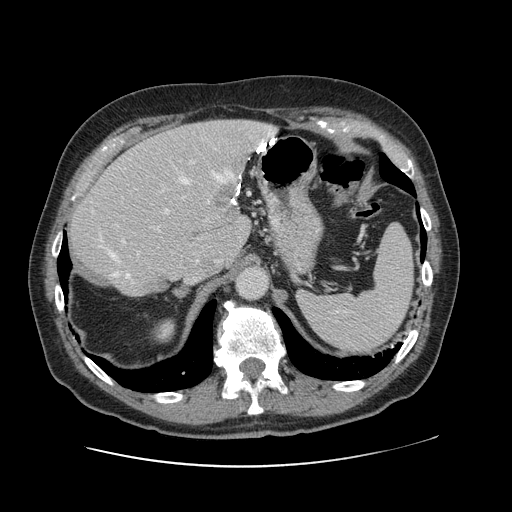
Contrast-enhanced abdominal CT, one axial slice; slice 82 of 138 in the series (ordered by position); 120 kVp; intravenous contrast given; soft-tissue window (W 400 / L 40 HU); 2.5 mm slice thickness; 512 × 512 image matrix. Male patient, age 71 years. From the clinical record (not read from this slice): diagnosis: colorectal cancer liver metastases, imaged before liver resection; multiple liver metastases: no; largest metastasis: 3.3 cm; chemotherapy before resection: no.
Outlined on this slice (expert manual segmentation):
- hepatic veins: bounding box (x1, y1, x2, y2) in pixels: (99, 139, 266, 282)
- liver: (69, 121, 272, 295)
- planned liver remnant (the part of the liver to remain after resection): (69, 151, 238, 296)
- portal vein (with intrahepatic branches): (120, 161, 196, 244)
- liver metastasis: (211, 184, 237, 214)